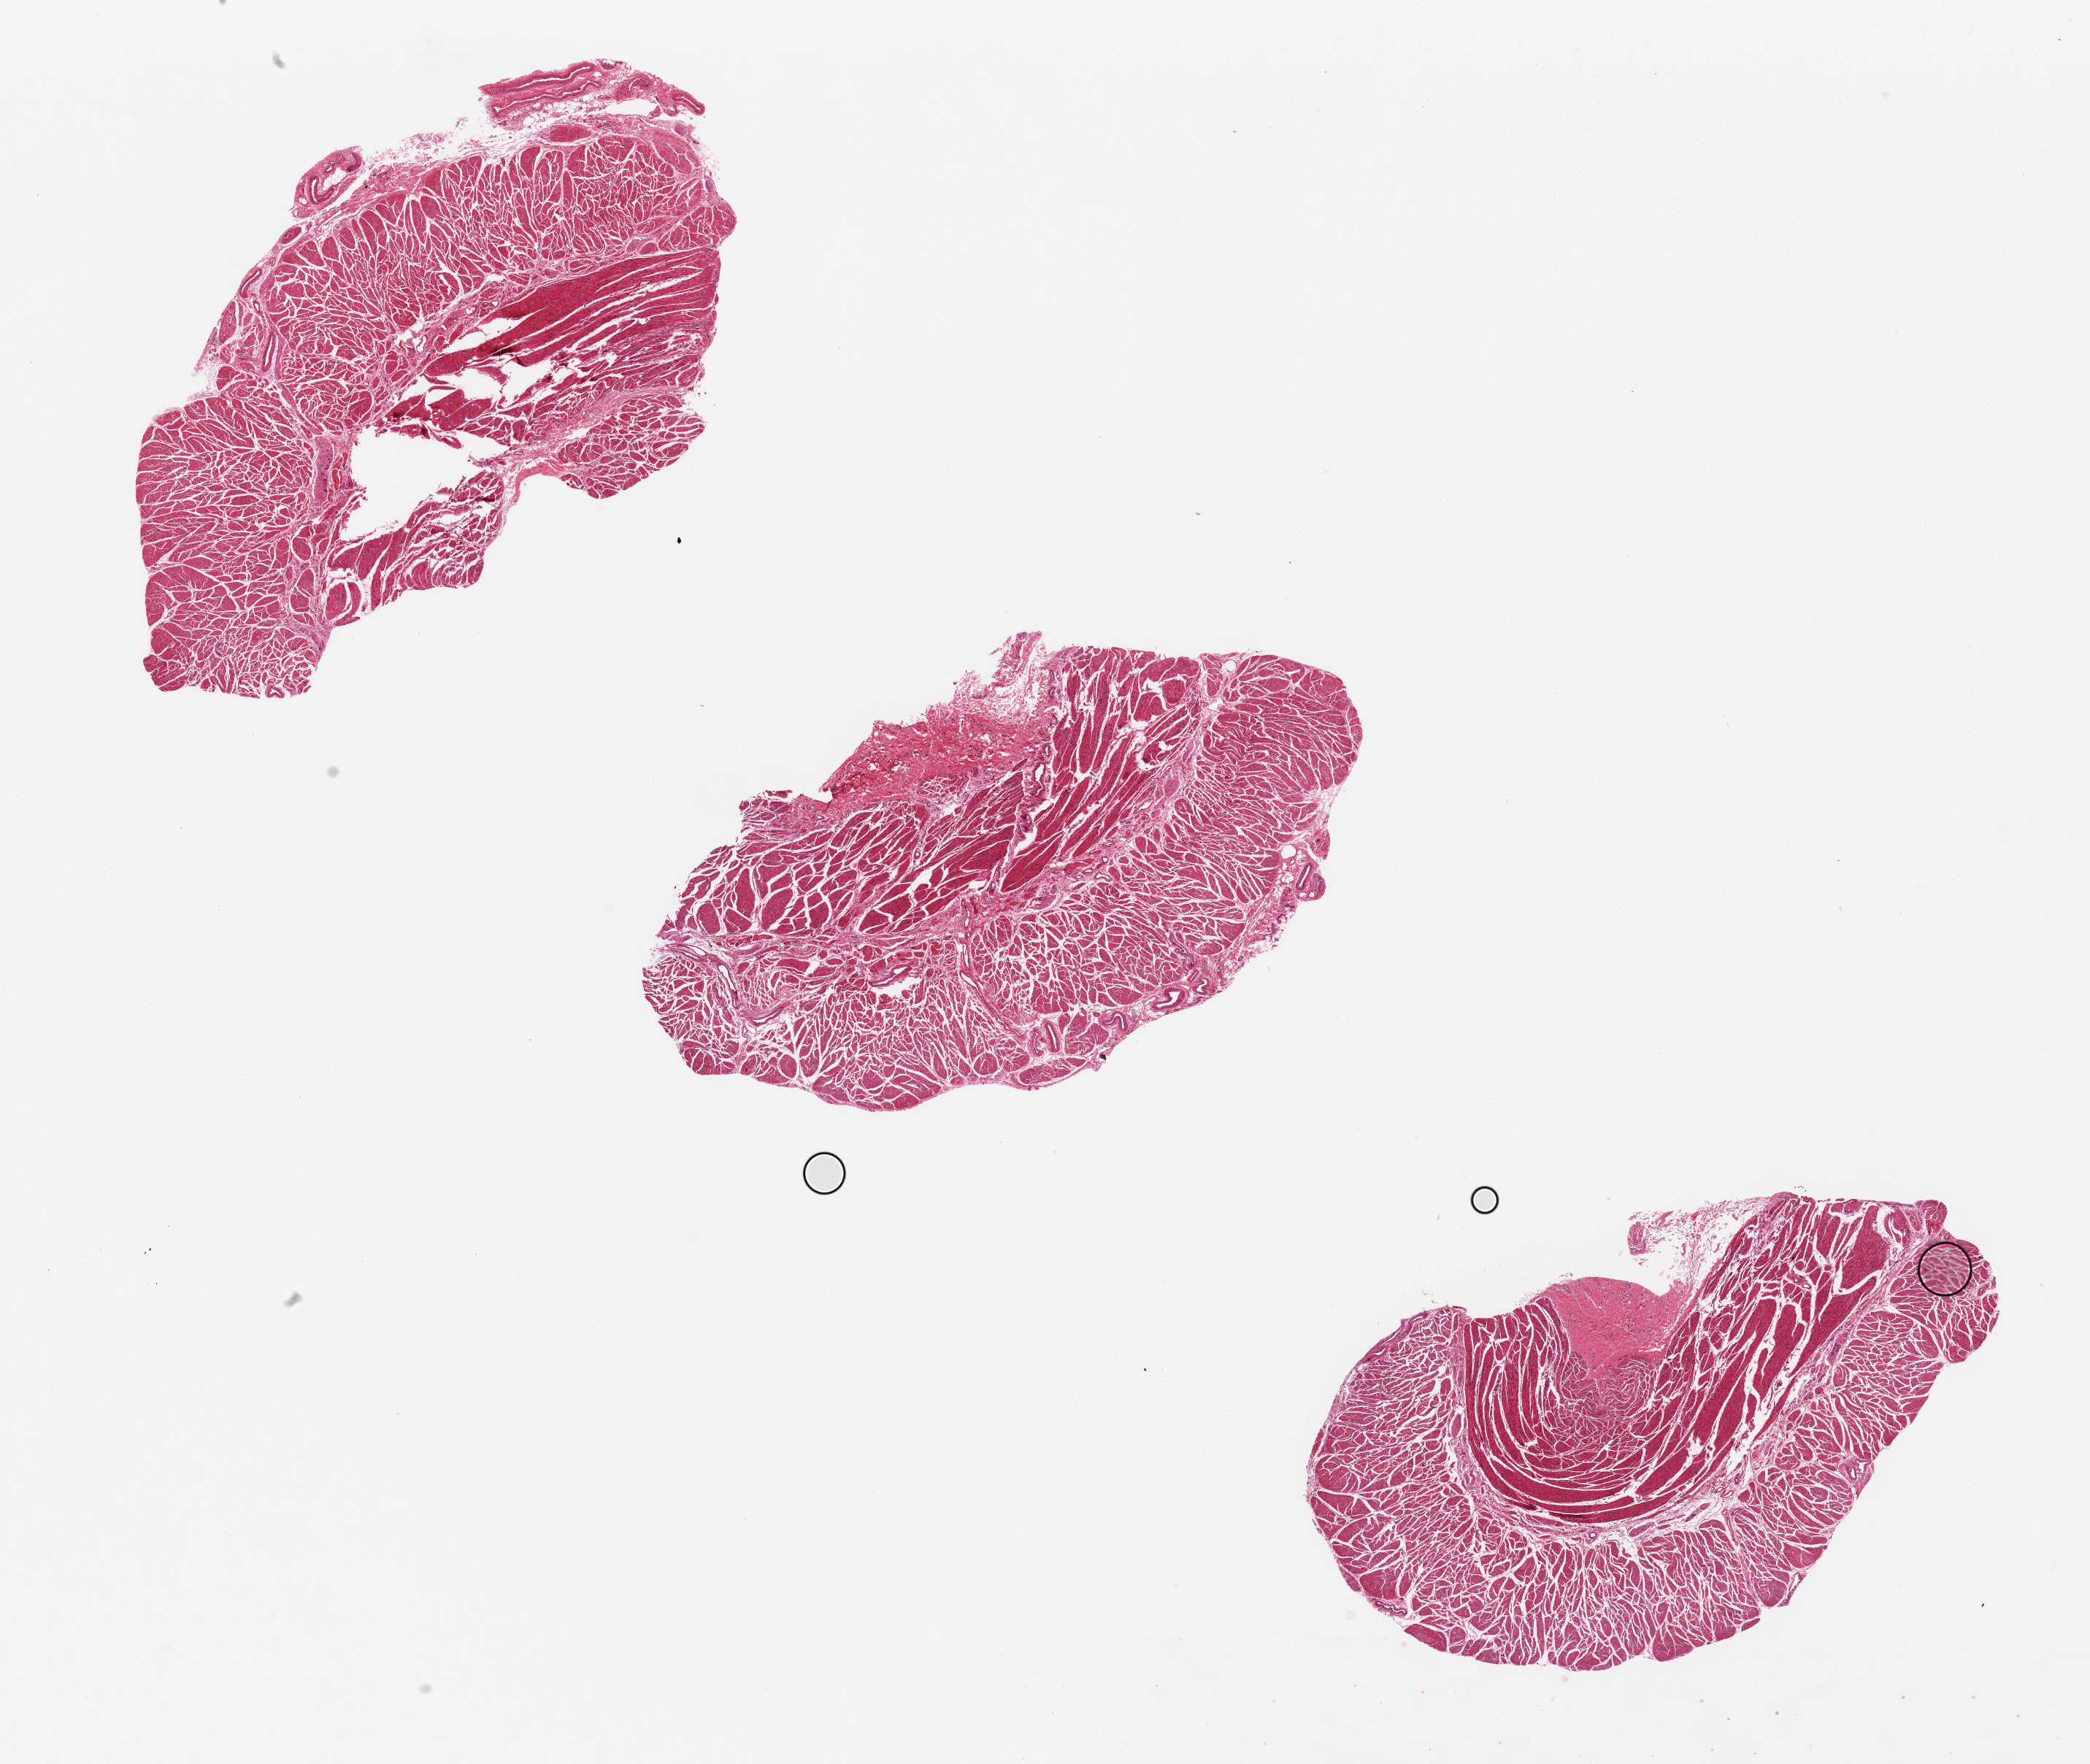
Hematoxylin and eosin (H&E) whole-slide image — shown as a low-resolution overview of the whole scanned area (about 22.6 x 19.1 mm, slide scanned at 20x); PAXgene-fixed paraffin-embedded (PFPE) section; sampled site (target tissue): esophageal muscle; donor tissue sample. Donor: male.
Pathologist's review note for this sample: Aliquots average 8 x 4mm.